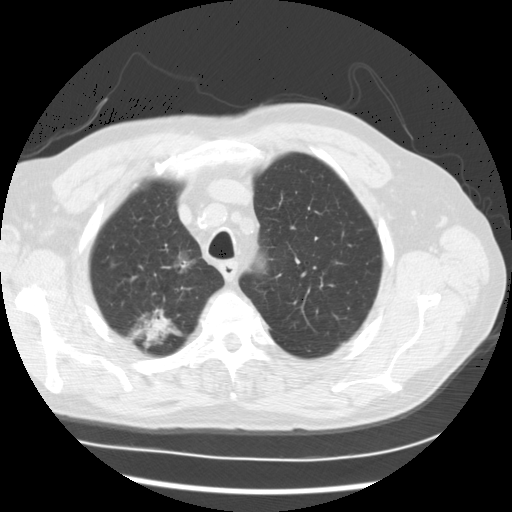
Low-dose screening chest CT, axial slice, first (baseline) screen, lung window (W 1500 / L -600 HU), 2.5 mm slice thickness. Male participant, aged 68 years at enrolment.
• Expert reader's lesion annotation, bounding box [x1, y1, x2, y2] px = [115, 291, 190, 361].
• The screening reader recorded 3 non-calcified nodules or masses ≥4 mm on this exam; which of them this box marks is not recorded.
• Participant outcome: lung cancer diagnosed 90 days after this screen — adenocarcinoma, NOS, right upper lobe, right lower lobe, well differentiated (G1), stage IV (AJCC 6th edition), 35 mm at pathology.